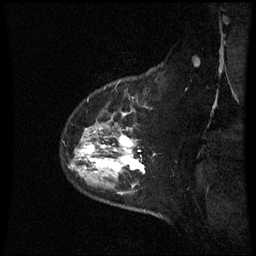
Breast MRI (dynamic contrast-enhanced), one sagittal slice. Slice 51 of 60 in the series (ordered by position). Dynamic contrast-enhanced series, image 2 of 3 at this slice position (ordered by acquisition). 1.5 T. TE 4.2 ms, TR 8.9 ms. 2.3 mm slice thickness. 256 × 256 image matrix, field of view 210 × 210 mm. Female patient, age 43 years. Case-level facts recorded for this patient, not image findings: setting: breast cancer imaged before/during neoadjuvant chemotherapy; receptor status: HER2-positive.
Outlined on this slice (semi-automatic segmentation, software-assisted and operator-edited):
- analysis volume of interest (the breast-tissue region the enhancement analysis was run in; not a lesion): bounding box <70,82,156,195> (left, top, right, bottom; pixels)
- tumour enhancement mask (voxels above the 70 % enhancement threshold inside the analysis volume of interest): <82,114,146,187>